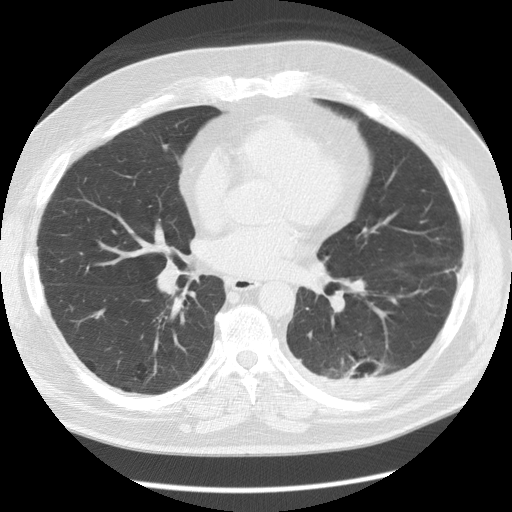
Low-dose screening chest CT, one axial slice; position 63 of 126 along the scan axis; reconstruction kernel STANDARD; lung window (W 1500 / L -600 HU); 2.5 mm slice thickness; 512 × 512 image matrix, field of view 370 × 370 mm.
Annotated regions visible in this slice (manually delineated by an expert):
- lesion 1 (tumor, lower lobe of left lung): bounding box (x1, y1, x2, y2) in pixels: (346, 359, 384, 379)